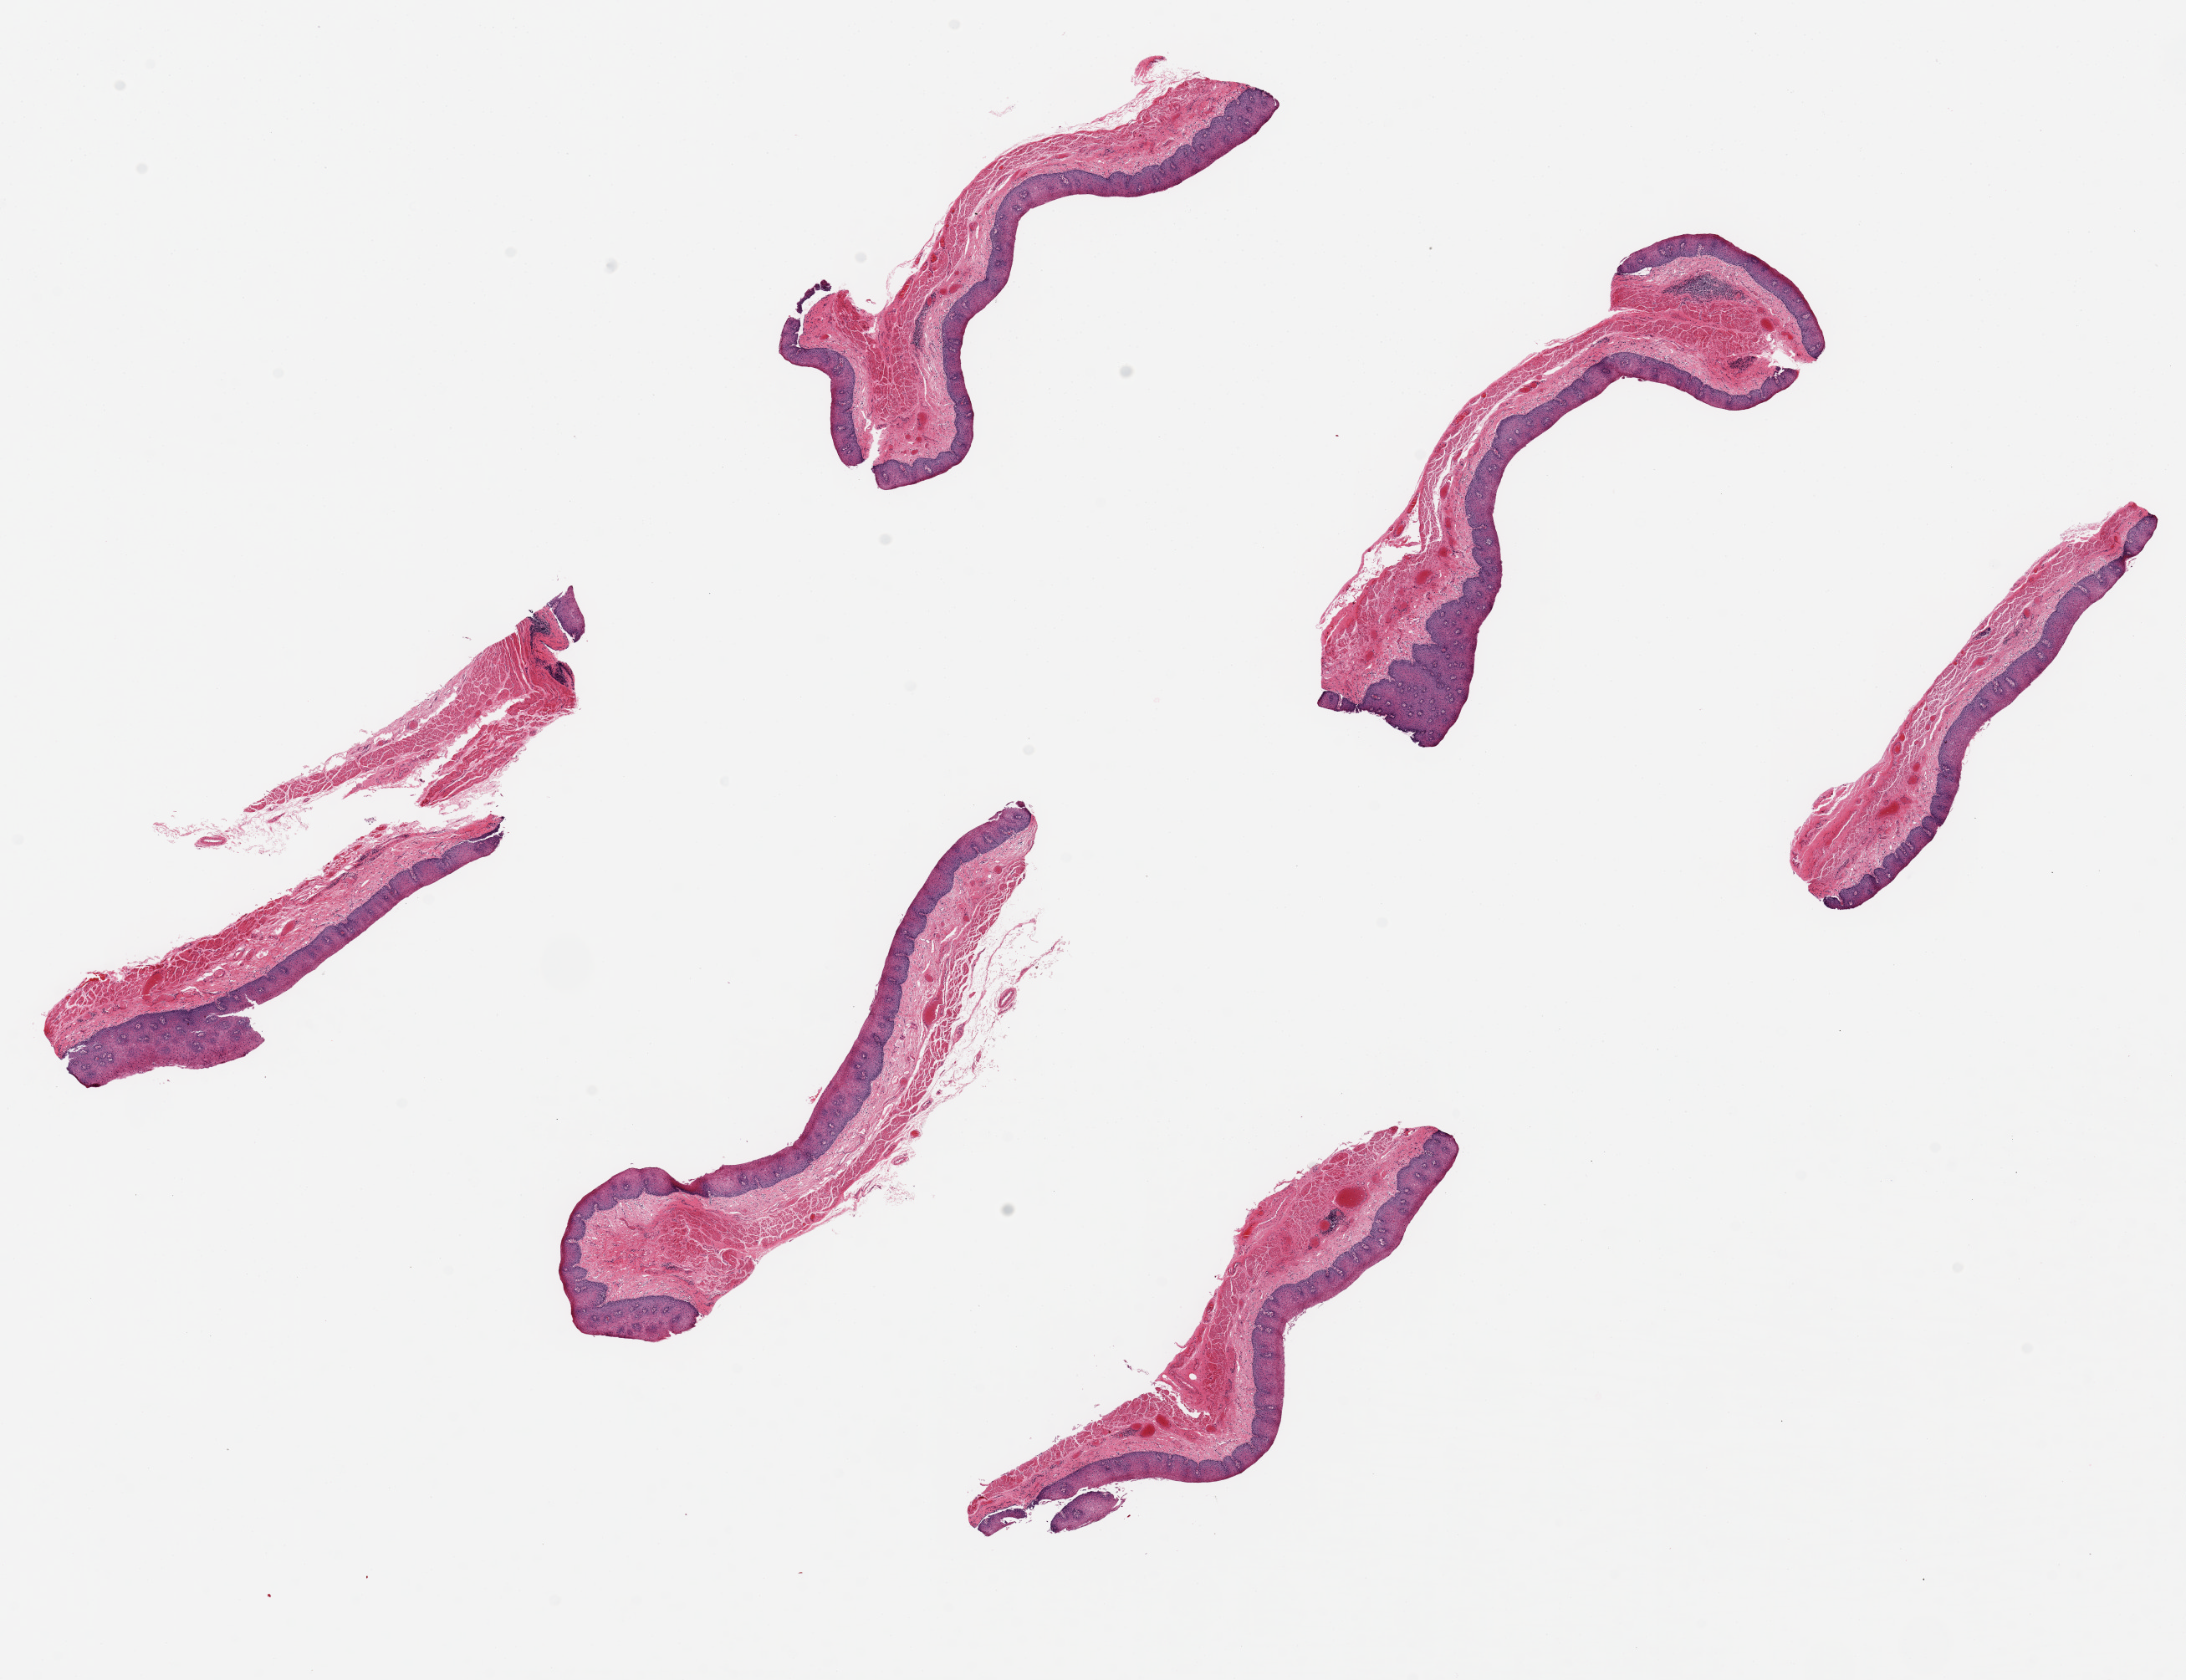
Whole-slide image, haematoxylin and eosin stain, shown as a low-resolution overview of the whole scanned area (about 20.7 x 15.9 mm, from a 20x scan), PAXgene-fixed paraffin-embedded (PFPE) section, sampled site (target tissue): esophageal mucous membrane, tissue donor sample. Donor sex: male.
* reviewer comment on this tissue sample: 6 ~6x1.2mm pieces; squamous mucosa is ~25-40% of thickness